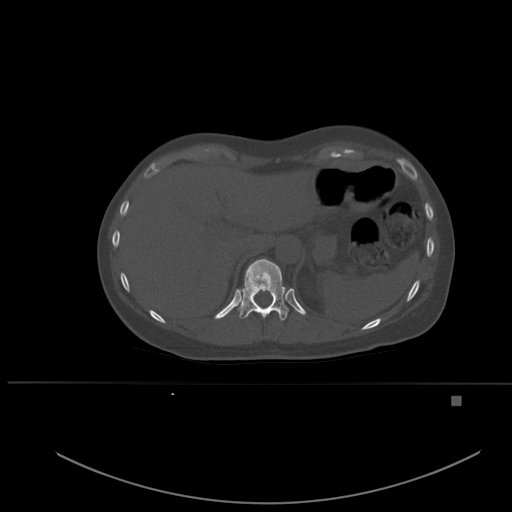
CT including the spine, one axial slice; position 274 of 651 along the scan axis; bone window (W 1800 / L 400 HU); 1.5 mm slice thickness; 512 × 512 image matrix, field of view 443 × 443 mm. Patient: female, 49 years. Case-level facts recorded for this patient, not image findings: primary cancer: breast.
Outlined on this slice (semi-automatic segmentation, software-assisted and operator-edited):
- T11 vertebra: box from (x=236, y=259) to (x=289, y=321) px